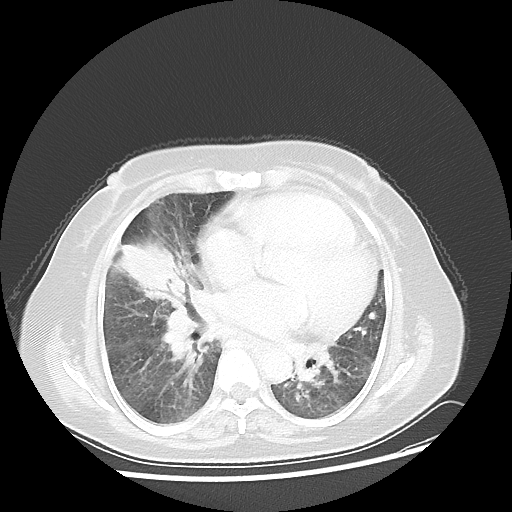
Chest CT, one axial slice; slice 21 of 45 in the series (ordered by position); lung window (W 1500 / L -600 HU); 512 × 512 image matrix. Patient: female, 67 years. From the clinical record (not read from this slice): clinical TNM (as recorded): T2a N3 M1a.
Outlined on this slice (bounding box drawn by a radiologist):
- lung tumour (recorded histology: adenocarcinoma): bounding box [x1, y1, x2, y2] px = [120, 242, 184, 305]